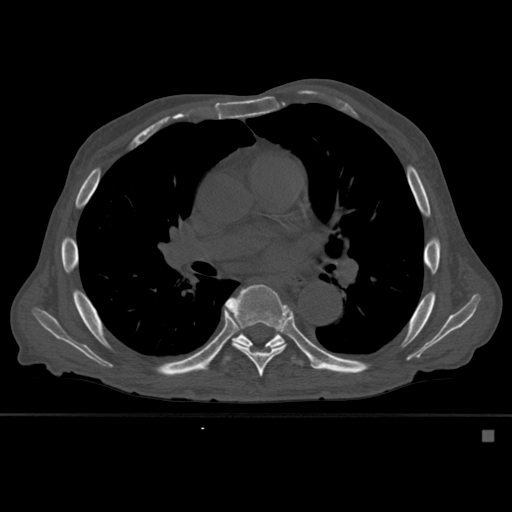
CT including the spine, one axial slice. Bone window (W 1800 / L 400 HU). 1.5 mm slice thickness. 512 × 512 image matrix, field of view 373 × 373 mm. Male patient, age 78 years. From the clinical record (not read from this slice): primary cancer: prostate.
Structures marked on this image (semi-automatically segmented with operator editing):
- T7 vertebra: bounding box (x1, y1, x2, y2) in pixels: (224, 284, 294, 377)
- T8 vertebra: (223, 331, 304, 366)